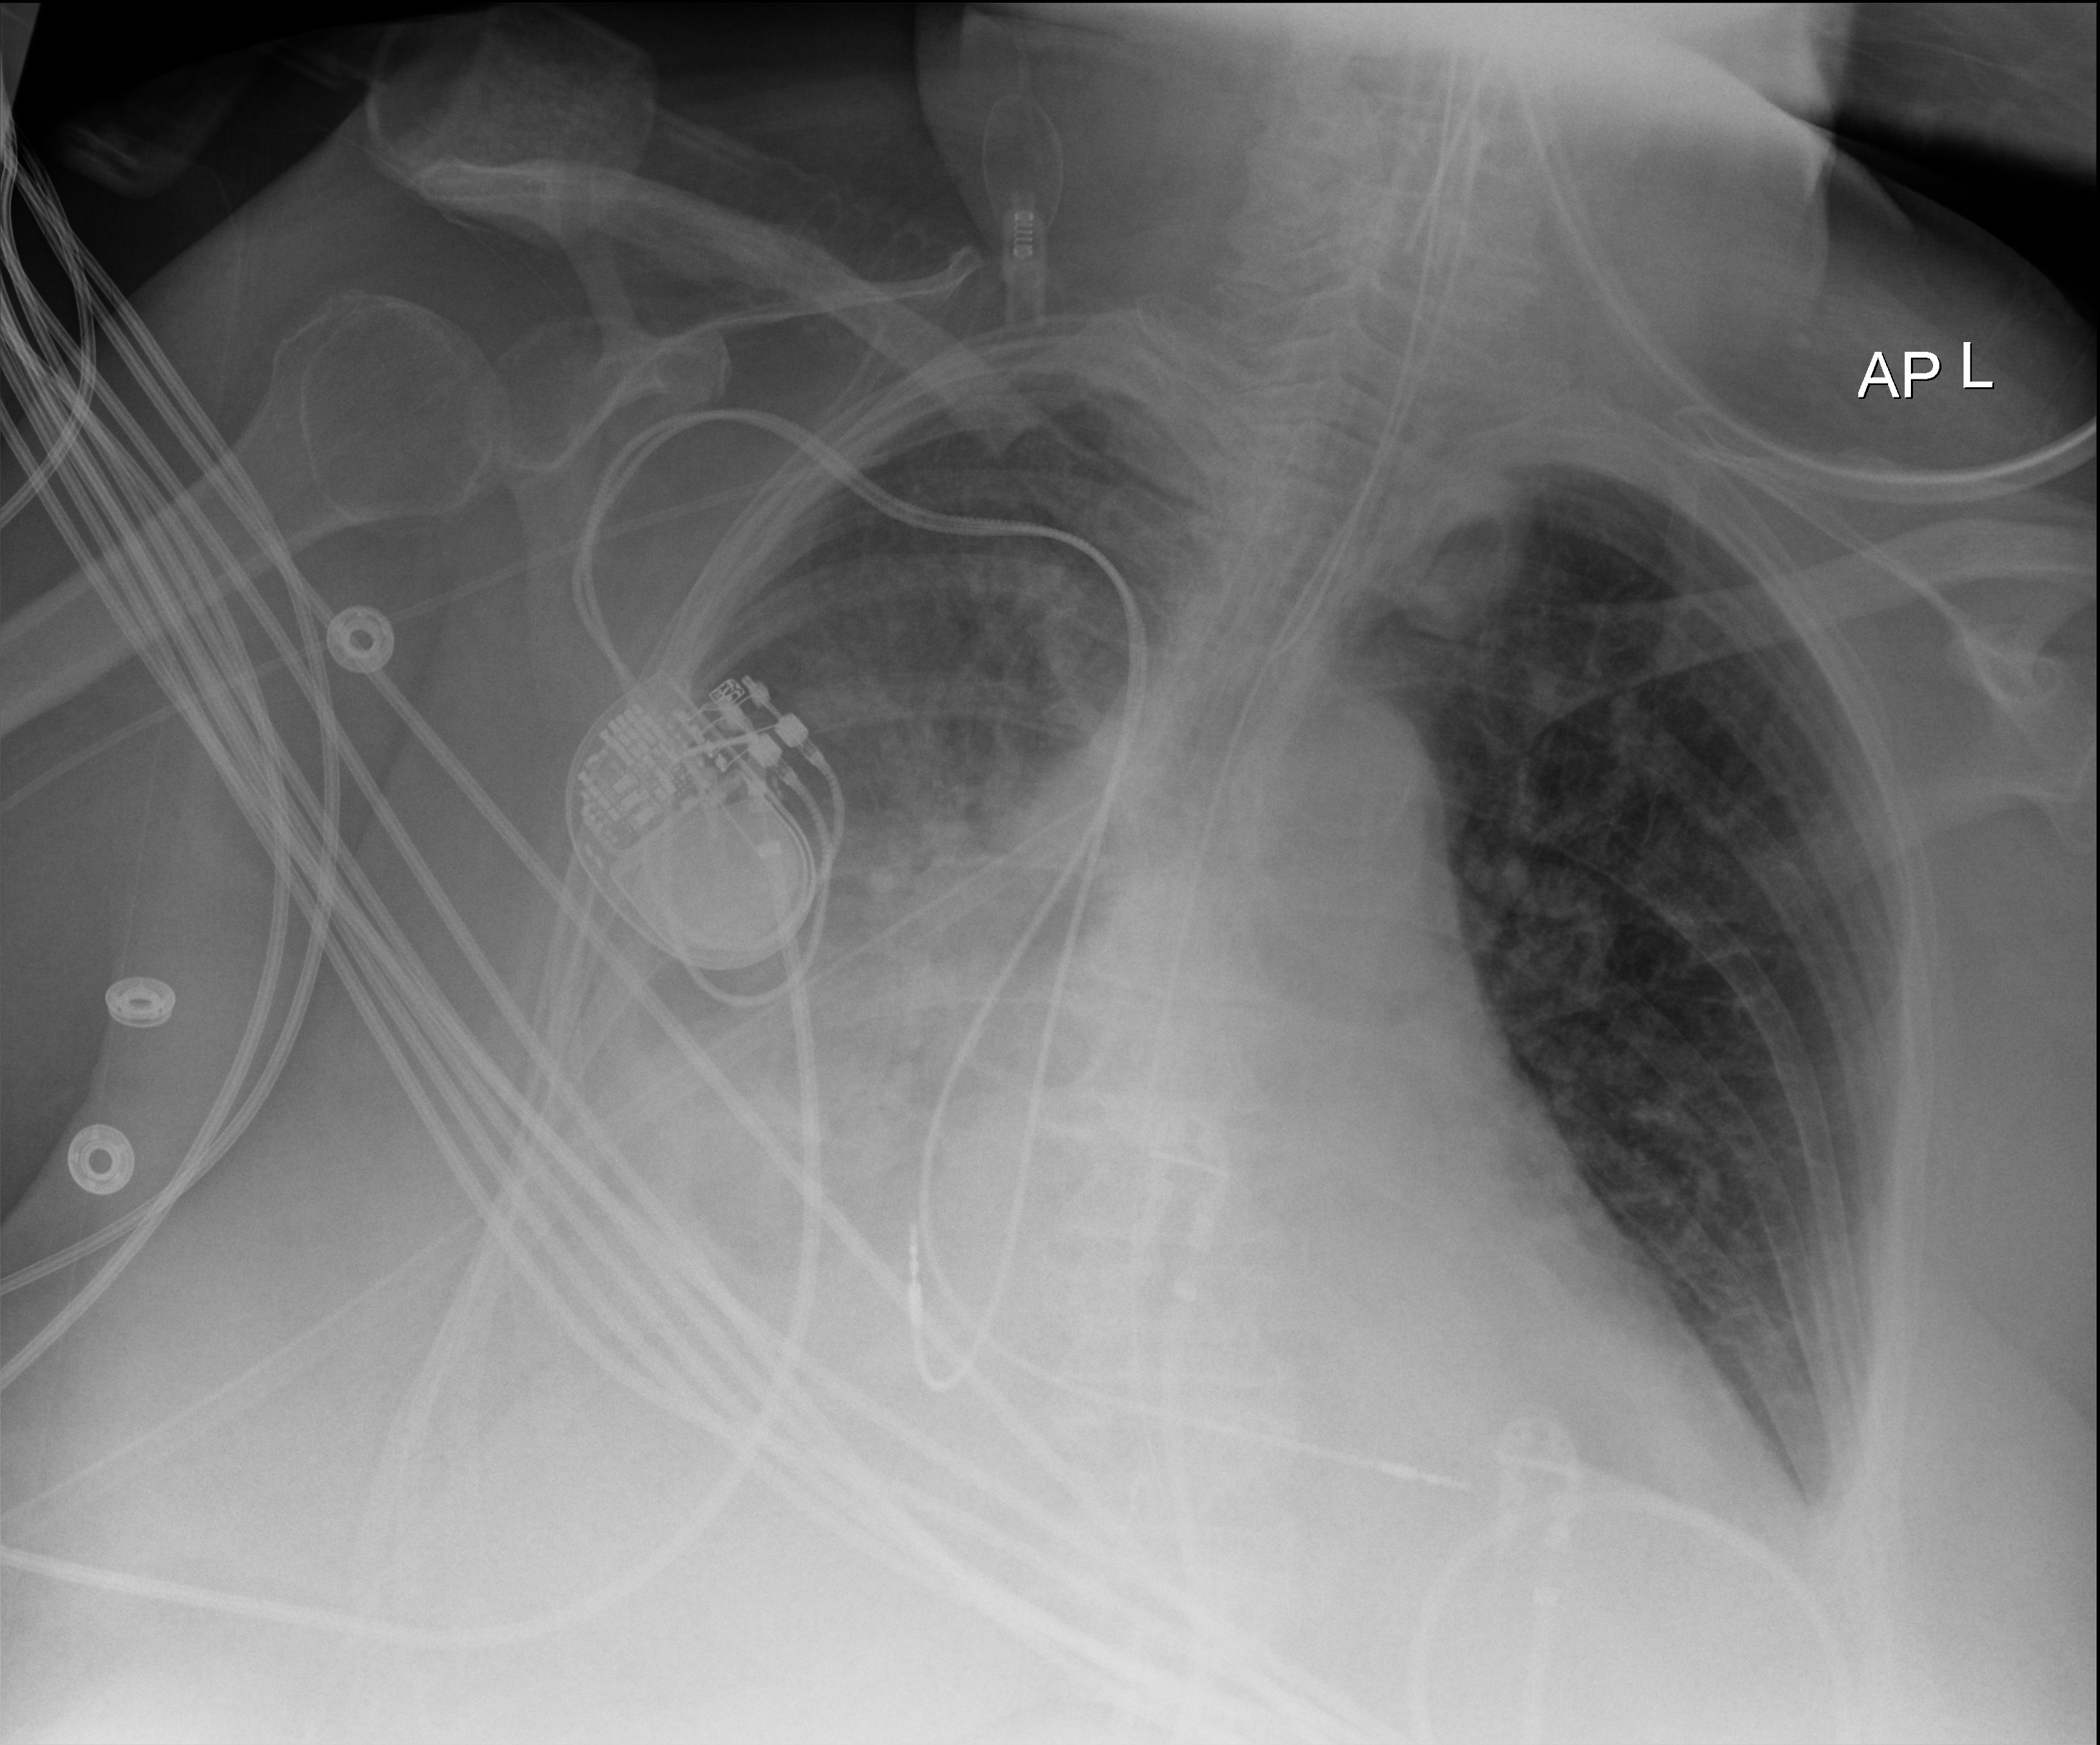
Portable chest radiograph. Female patient hospitalised with COVID-19, age 75–90 years.
Admission-level facts for this patient (not findings on this image; timing relative to this image not recorded): admitted to intensive care during this hospital stay: yes; mechanically ventilated during this hospital stay: yes.